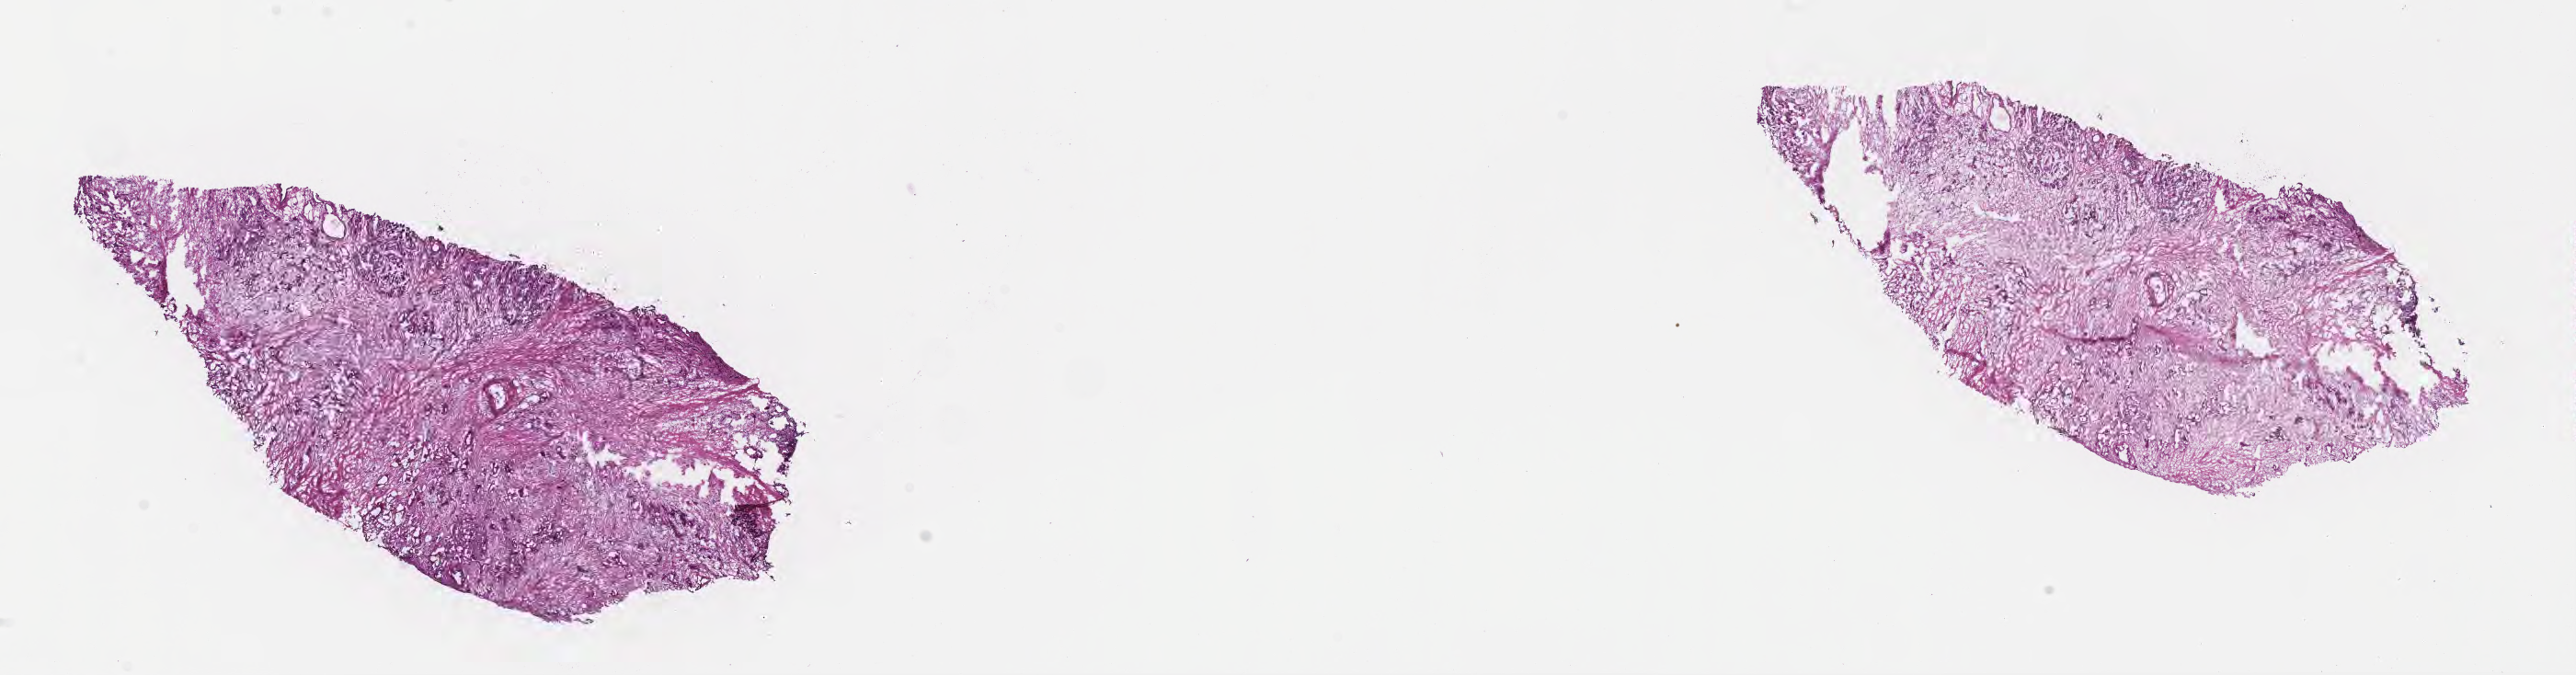
H&E whole-slide image — shown as a low-resolution overview of the whole scanned area (about 22.6 x 5.9 mm). Frozen section (tissue freezing medium). Primary tumor. Anatomic site: head of pancreas. Male, age 75 years at initial diagnosis. Tumor grade: G3 (poorly differentiated). Pathologist review of this section (percent, as recorded): tumor cells 30%, tumor nuclei 40%, stromal cells 60%, necrosis 0%, normal cells 10%. Infiltration values recorded for this section: lymphocyte infiltration 0%, monocyte infiltration 0%, neutrophil infiltration 0%.
Histologic diagnosis: Infiltrating duct carcinoma, NOS. Section: bottom of the tissue portion. AJCC pathologic stage: Stage III.